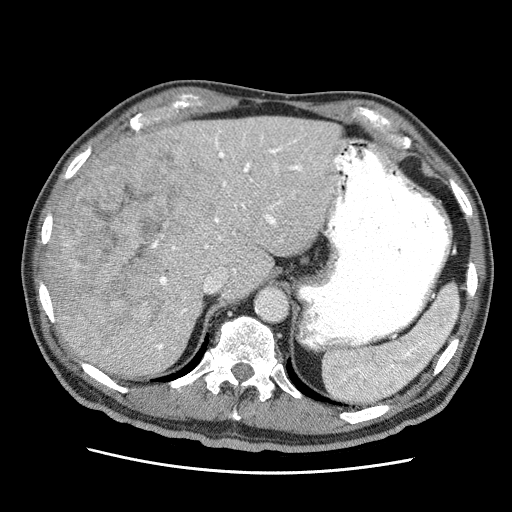
Contrast-enhanced abdominal CT (liver protocol), one axial slice; slice 42 of 75 in the series (ordered by position); reconstruction kernel STANDARD; soft-tissue window (W 400 / L 40 HU); 2.5 mm slice thickness; 512 × 512 image matrix, field of view 360 × 360 mm. Case-level facts recorded for this patient, not image findings: diagnosis: hepatocellular carcinoma (patient treated with transarterial chemoembolisation; whether this scan precedes or follows treatment is not stated here); TNM stage (as recorded): Stage-IIIA; Child-Pugh class: A; tumour differentiation: well differentiated; tumour nodularity: multinodular.
Structures marked on this image (semi-automatic segmentation, software-assisted and operator-edited):
- liver parenchyma outside the tumour (the mass and vessels are separate outlines, so this box may not span the whole liver): bounding box (x1, y1, x2, y2) in pixels: (44, 116, 342, 376)
- mass: (50, 141, 225, 351)
- liver vessels: (131, 130, 316, 355)